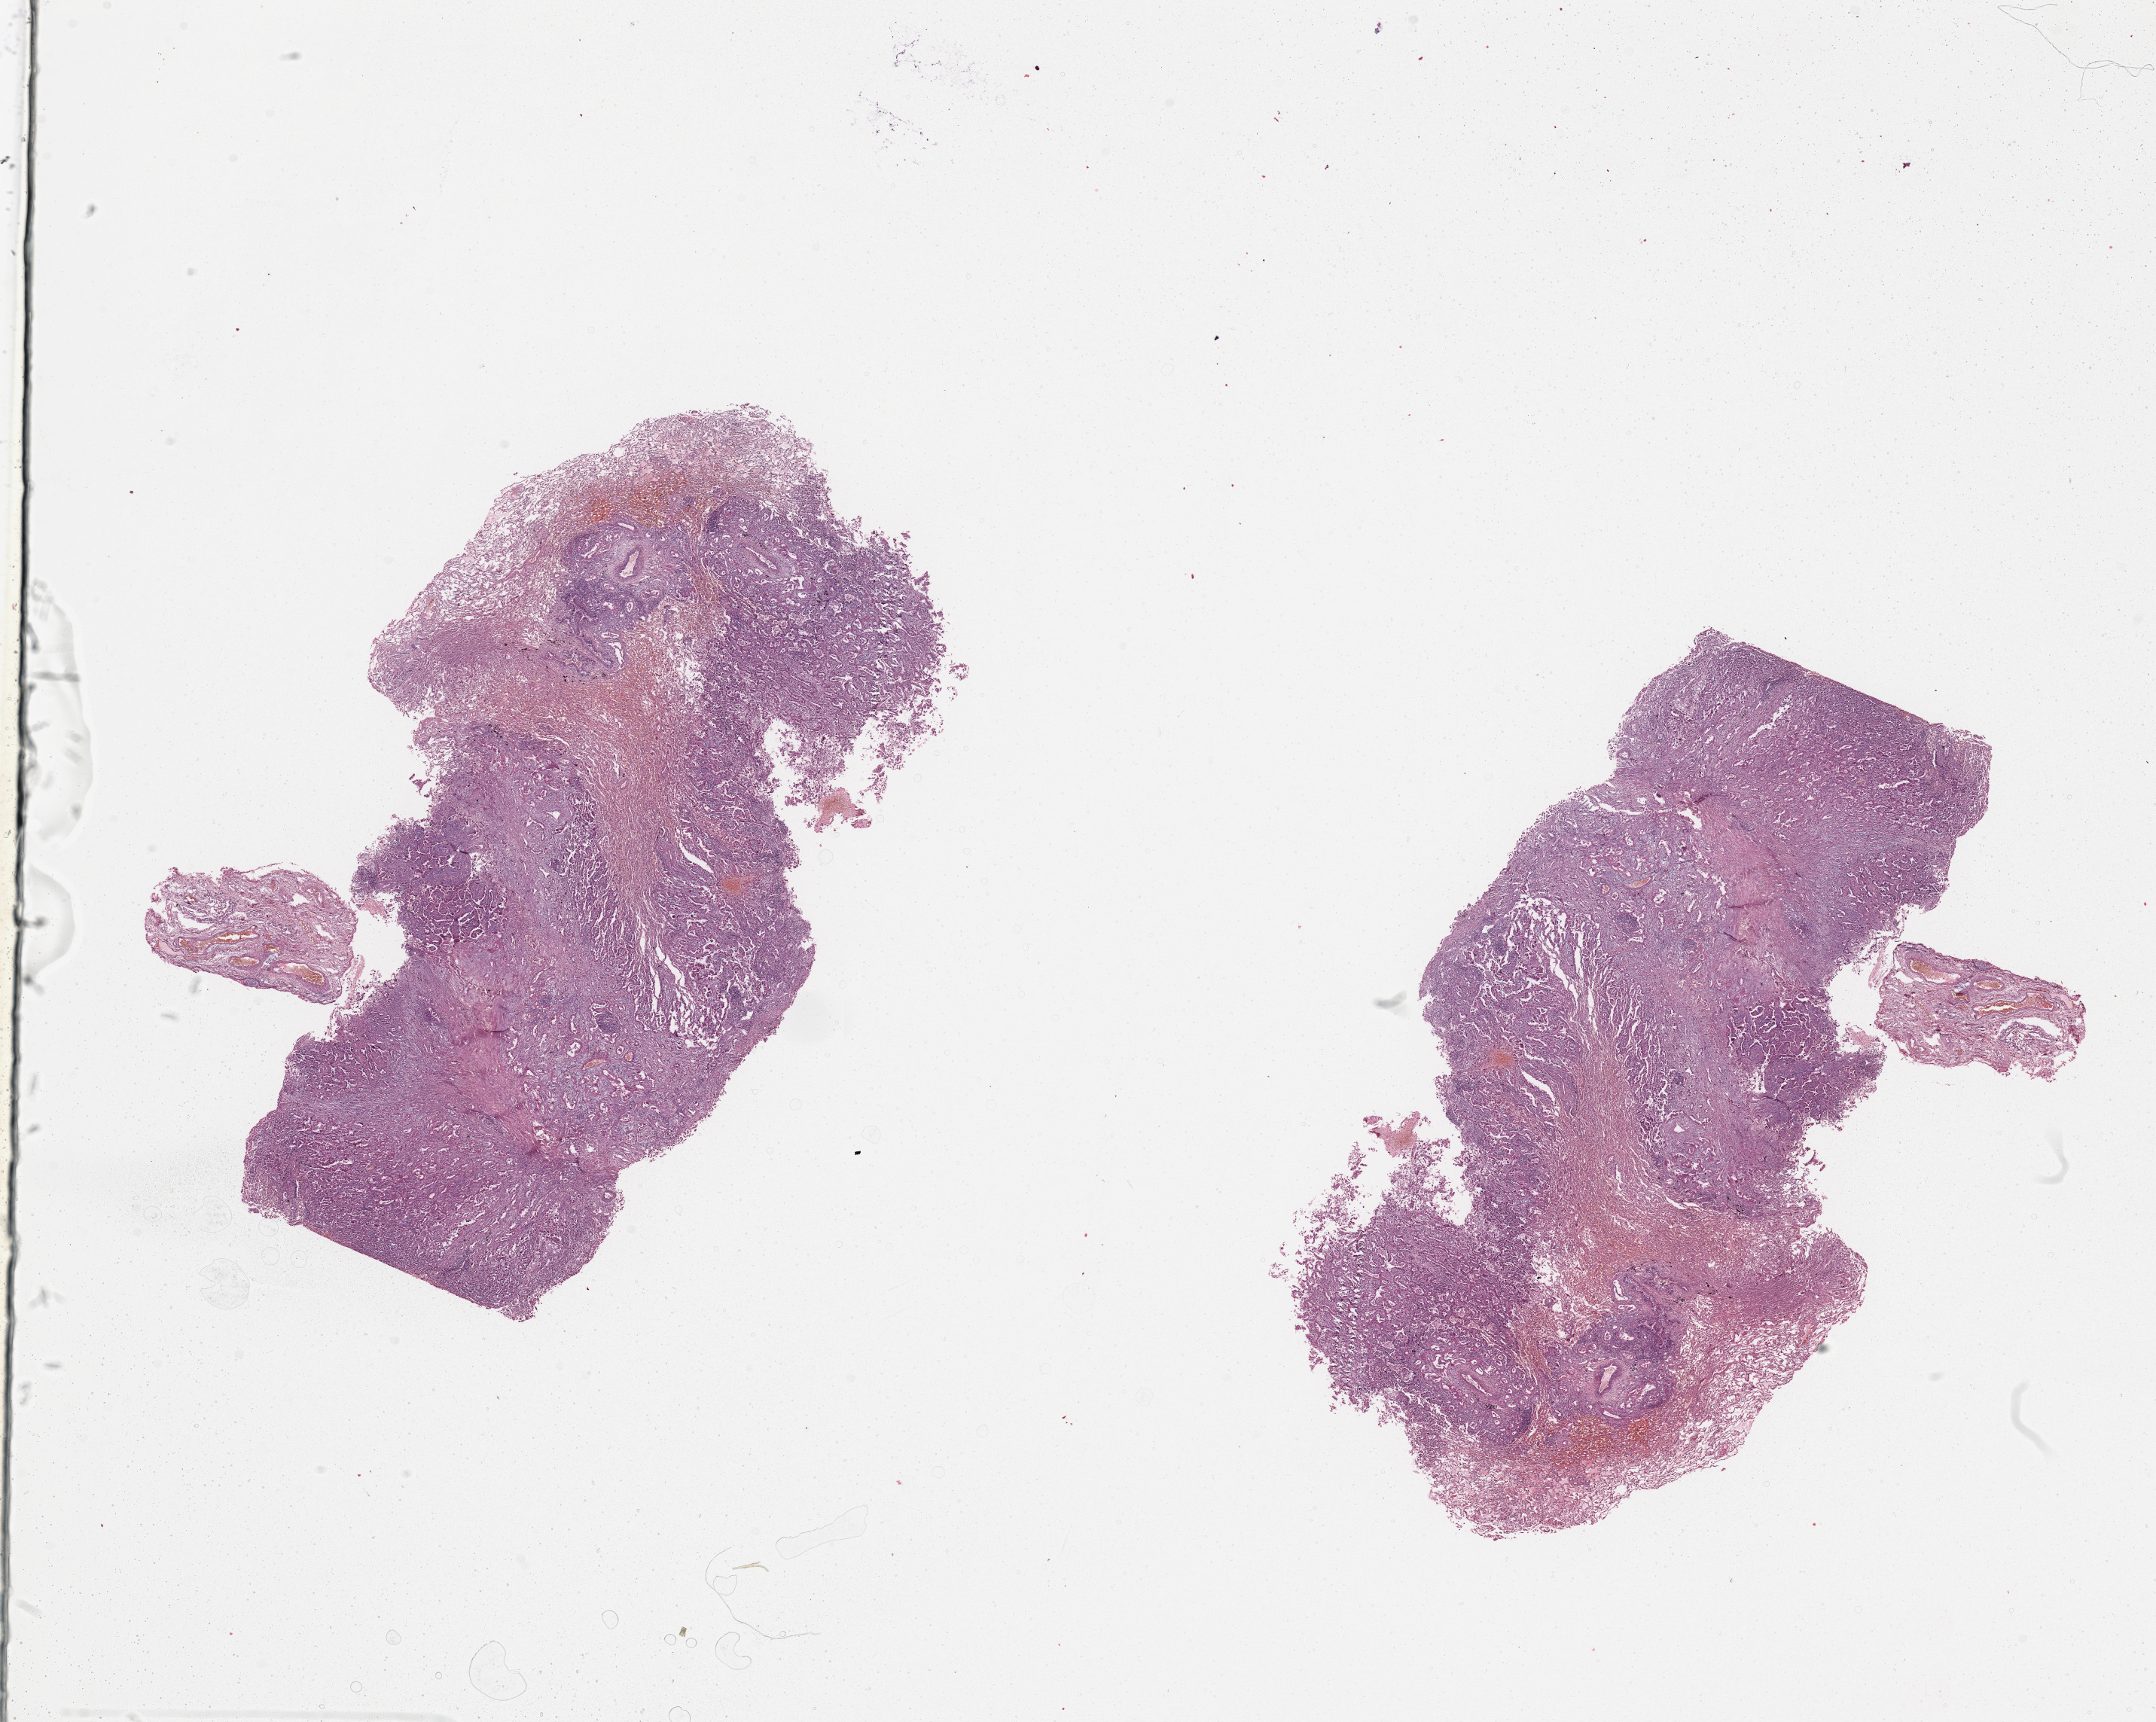
Digitized H&E-stained tissue section (whole slide), a low-resolution overview of the entire scanned area, about 22.6 x 18.1 mm; tumour tissue sample, lung. Patient: female, age 63 years. Histologic grade: G2 (moderately differentiated).
AJCC pathologic stage: IB. Diagnosis: Adenocarcinoma, NOS. Primary tumour site (as recorded): right upper lobe.